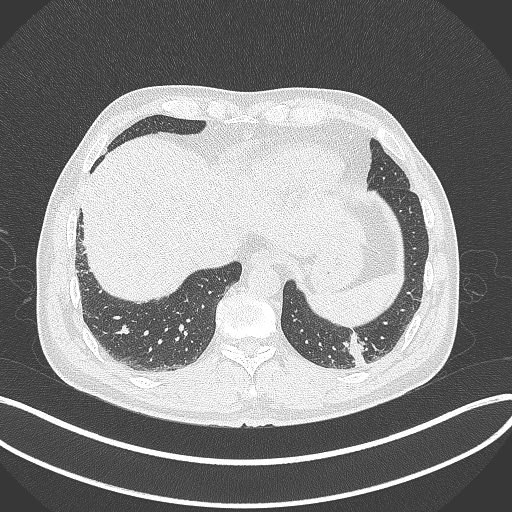
Chest CT, one axial slice; slice 54 of 300 in the series (ordered by position); 120 kVp; lung window (W 1500 / L -600 HU); 1 mm slice thickness; 512 × 512 image matrix. Patient: male, 54 years. Case-level facts recorded for this patient, not image findings: clinical TNM (as recorded): T1c N0 M1; histopathological grade: G3.
Structures marked on this image (bounding box drawn by a radiologist):
- lung tumour (recorded histology: adenocarcinoma): bounding box <340,333,370,372> (left, top, right, bottom; pixels)